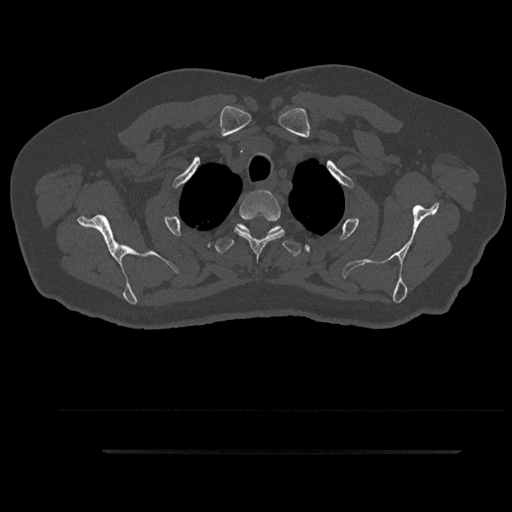
CT including the spine, one axial slice. Position 747 of 797 along the scan axis. Reconstruction kernel Br40s/3. 120 kVp. Bone window (W 1800 / L 400 HU). 0.5 mm slice thickness. 512 × 512 image matrix. Male patient, age 63 years. From the clinical record (not read from this slice): primary cancer: renal; vertebrae with lytic lesions (as recorded): T8.
Structures marked on this image (semi-automatic segmentation, software-assisted and operator-edited):
- T2 vertebra: bounding box (x1, y1, x2, y2) in pixels: (234, 190, 285, 259)
- T3 vertebra: (215, 224, 302, 256)